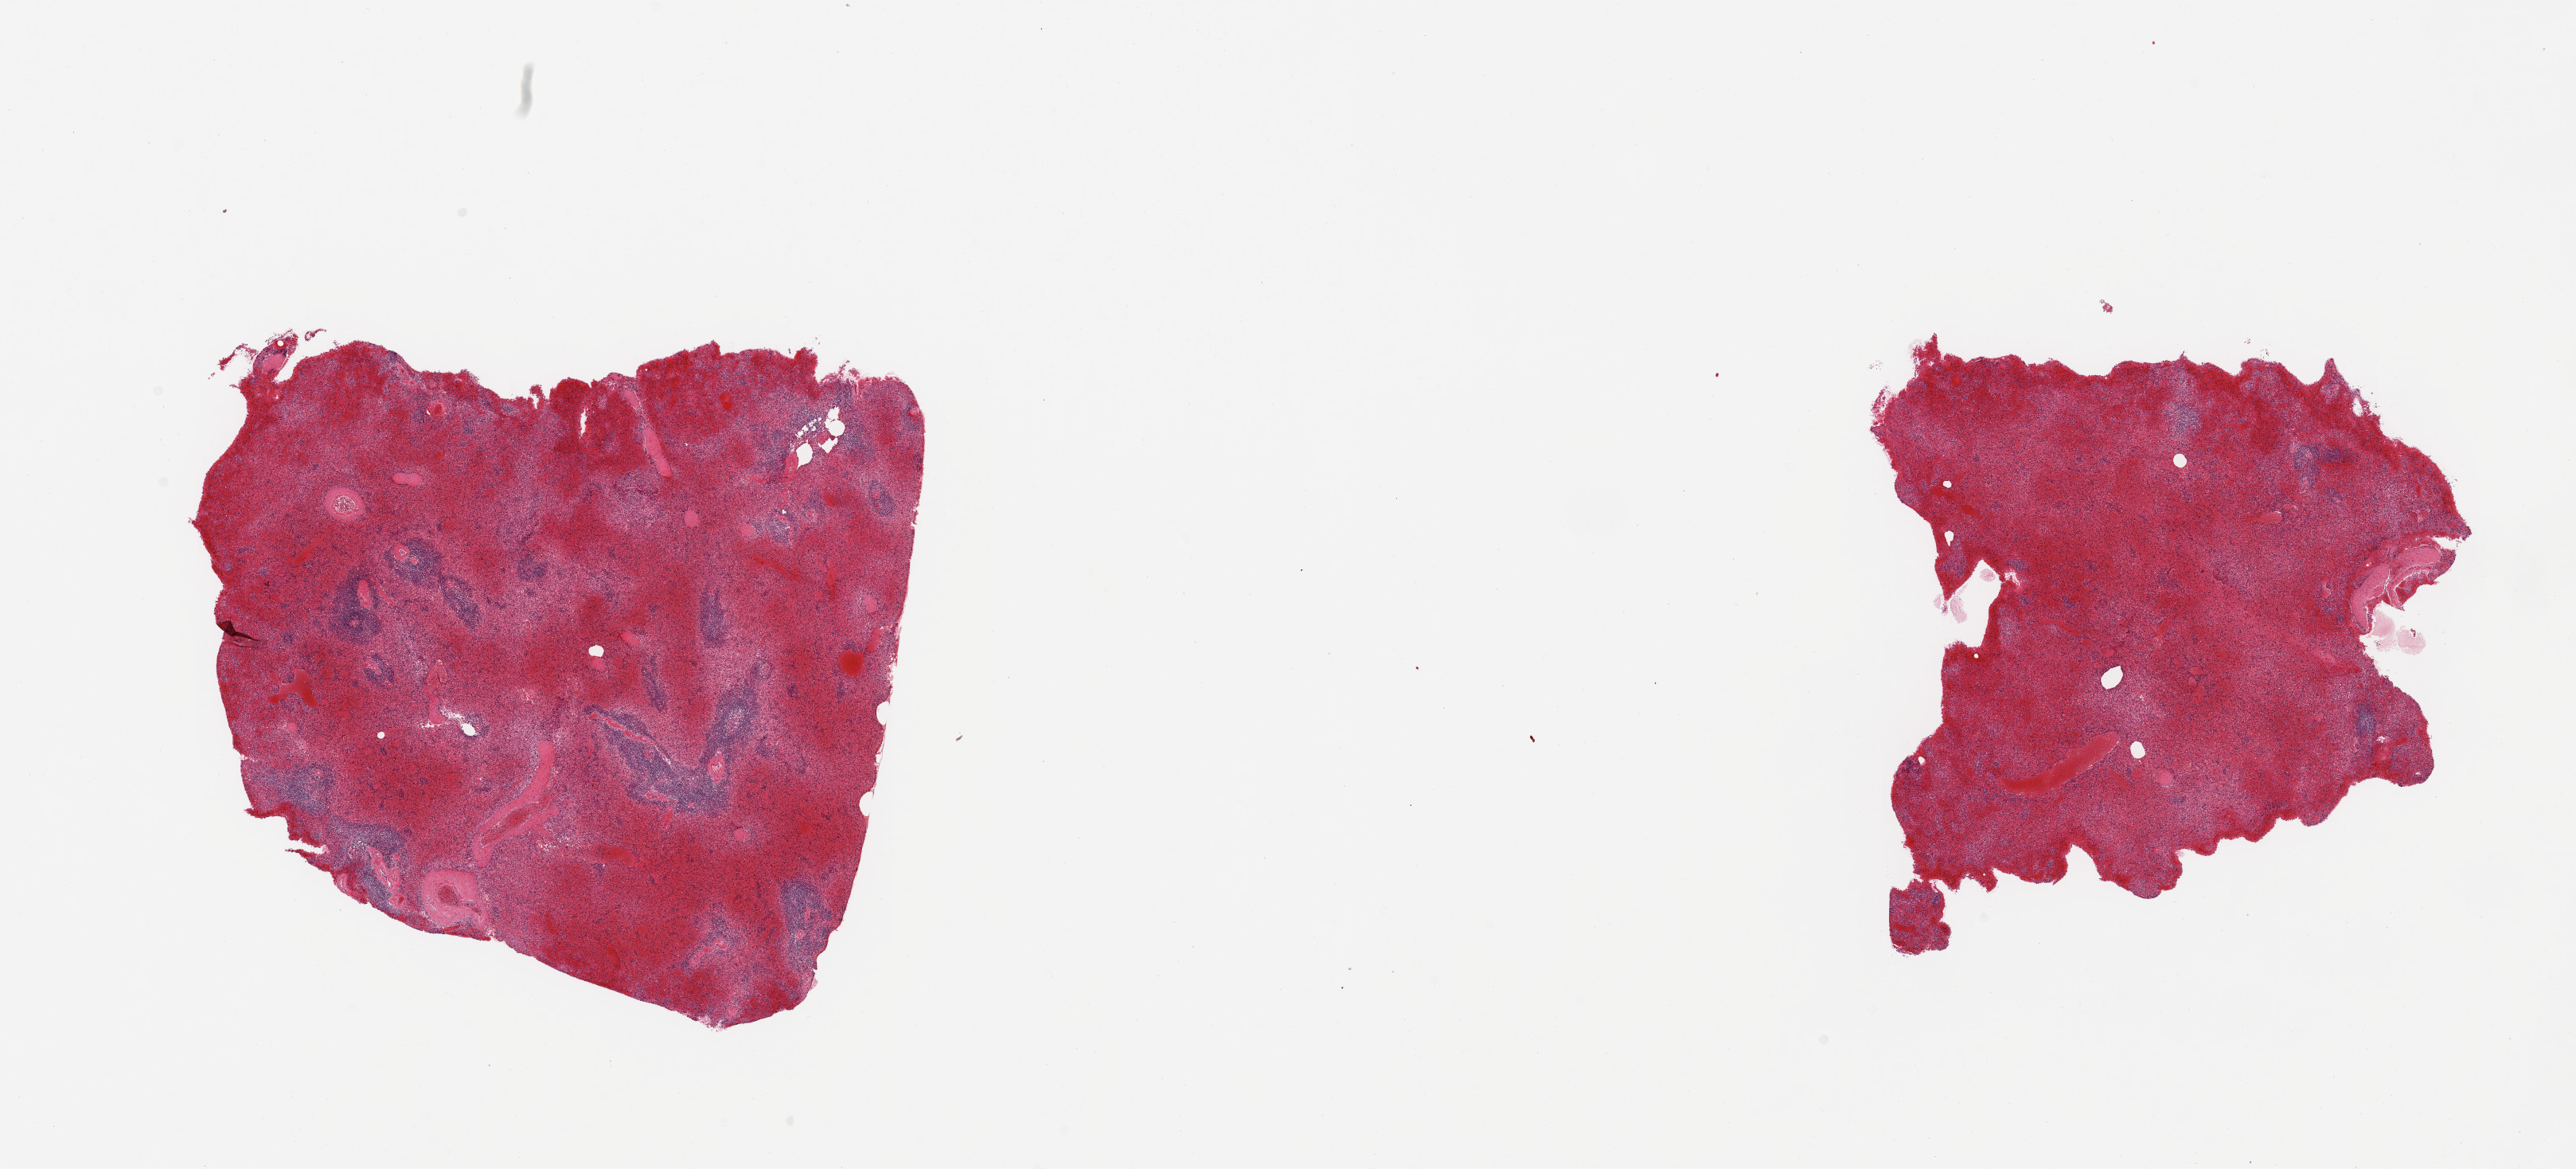
Whole-slide image, H&E stain, low-resolution overview of the scanned area, about 25.6 x 11.6 mm; PAXgene-fixed, paraffin-embedded tissue; sampled site (target tissue): spleen; donor tissue sample. Male donor.
Review note (as recorded): 2 pieces; congested.